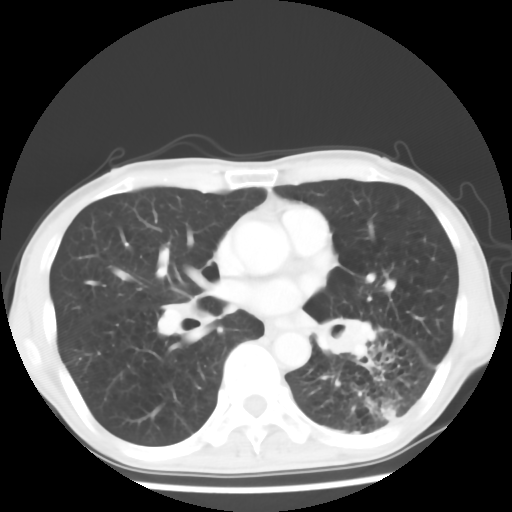
Chest CT, one axial slice; position 31 of 64 along the scan axis; reconstruction kernel STANDARD; 120 kVp; lung window (W 1500 / L -600 HU); 5 mm slice thickness; 512 × 512 image matrix, field of view 313 × 313 mm. Patient: male, 68 years. Case-level facts recorded for this patient, not image findings: clinical TNM (as recorded): T4 N0 M0.
Annotated regions visible in this slice (rectangle marked by the reading radiologist):
- lung tumour (recorded histology: squamous cell carcinoma): bounding box <312,319,389,387> (left, top, right, bottom; pixels)